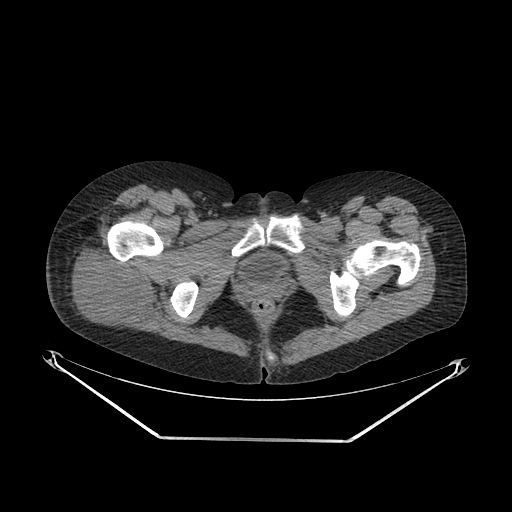
CT of an extremity soft-tissue mass (from a PET/CT study), one axial slice. Position 42 of 267 along the scan axis. Reconstruction kernel SOFT. 140 kVp. Soft-tissue window (W 400 / L 40 HU). 3.75 mm slice thickness. 512 × 512 image matrix, field of view 500 × 500 mm. Female patient. From the clinical record (not read from this slice): histological type: epithelioid sarcoma with vascular differentiation; site of the primary tumour: right buttock.
Annotated regions visible in this slice (expert contour drawn on MRI and transferred to this co-registered scan by the dataset authors):
- gross tumour volume (mass): bounding box [x1, y1, x2, y2] px = [66, 244, 156, 334]